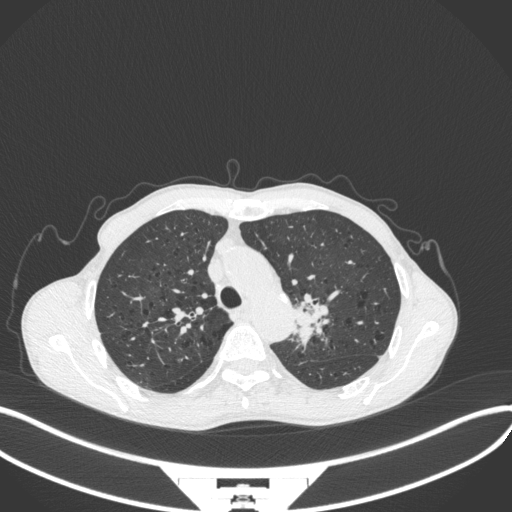
Chest CT, one axial slice; slice 308 of 394 in the series (ordered by position); 120 kVp; lung window (W 1500 / L -600 HU); 512 × 512 image matrix, field of view 400 × 400 mm. Patient: male, 65 years. From the clinical record (not read from this slice): clinical TNM (as recorded): T2b N0 M0; histopathological grade: G2.
Structures marked on this image (bounding box drawn by a radiologist):
- lung tumour (recorded histology: adenocarcinoma): bounding box (x1, y1, x2, y2) in pixels: (292, 290, 329, 356)